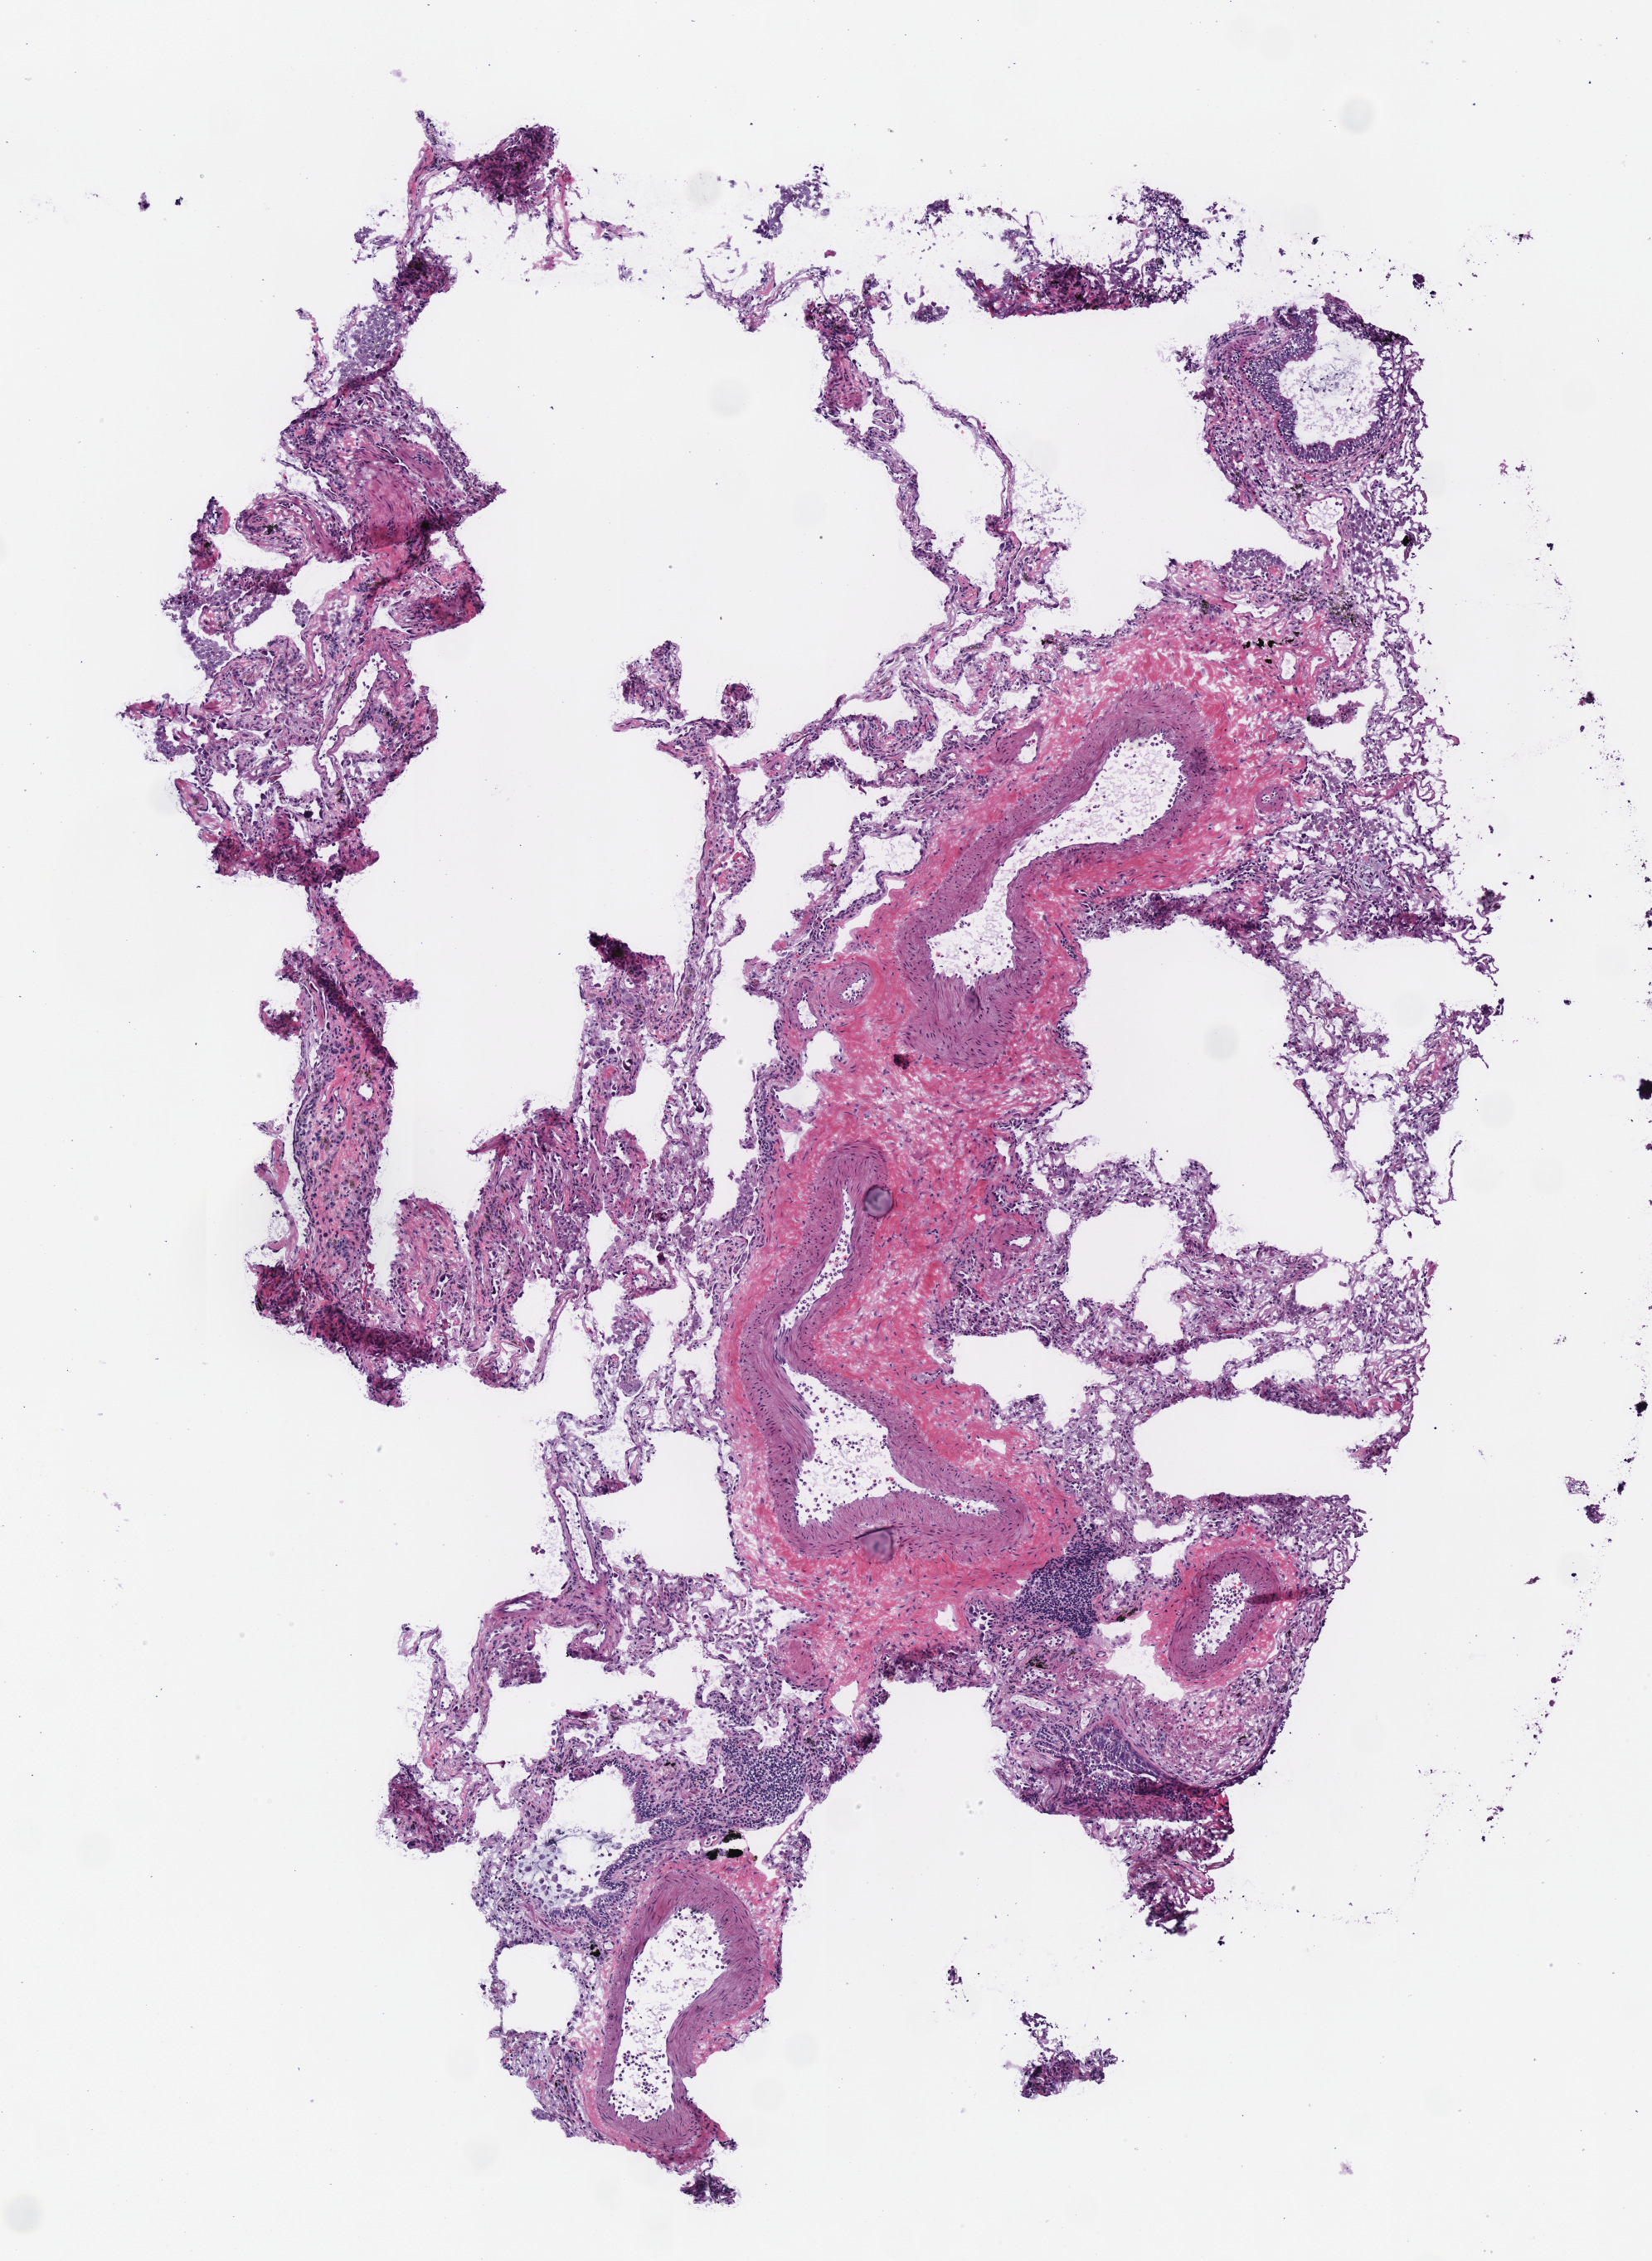
Whole-slide histology image, H&E, a low-resolution overview of the entire scanned area, about 3.9 x 5.4 mm (from a 40x scan), frozen section from the top of the tissue portion, solid tissue normal (non-tumour tissue) sample from the lung. Male, age 75 years at initial diagnosis. Infiltration values recorded for this section: lymphocyte infiltration 5%, monocyte infiltration 10%.
This section: solid tissue normal (non-tumour) sample from the same patient. Patient diagnosis: Squamous cell carcinoma, NOS (upper lobe, lung).